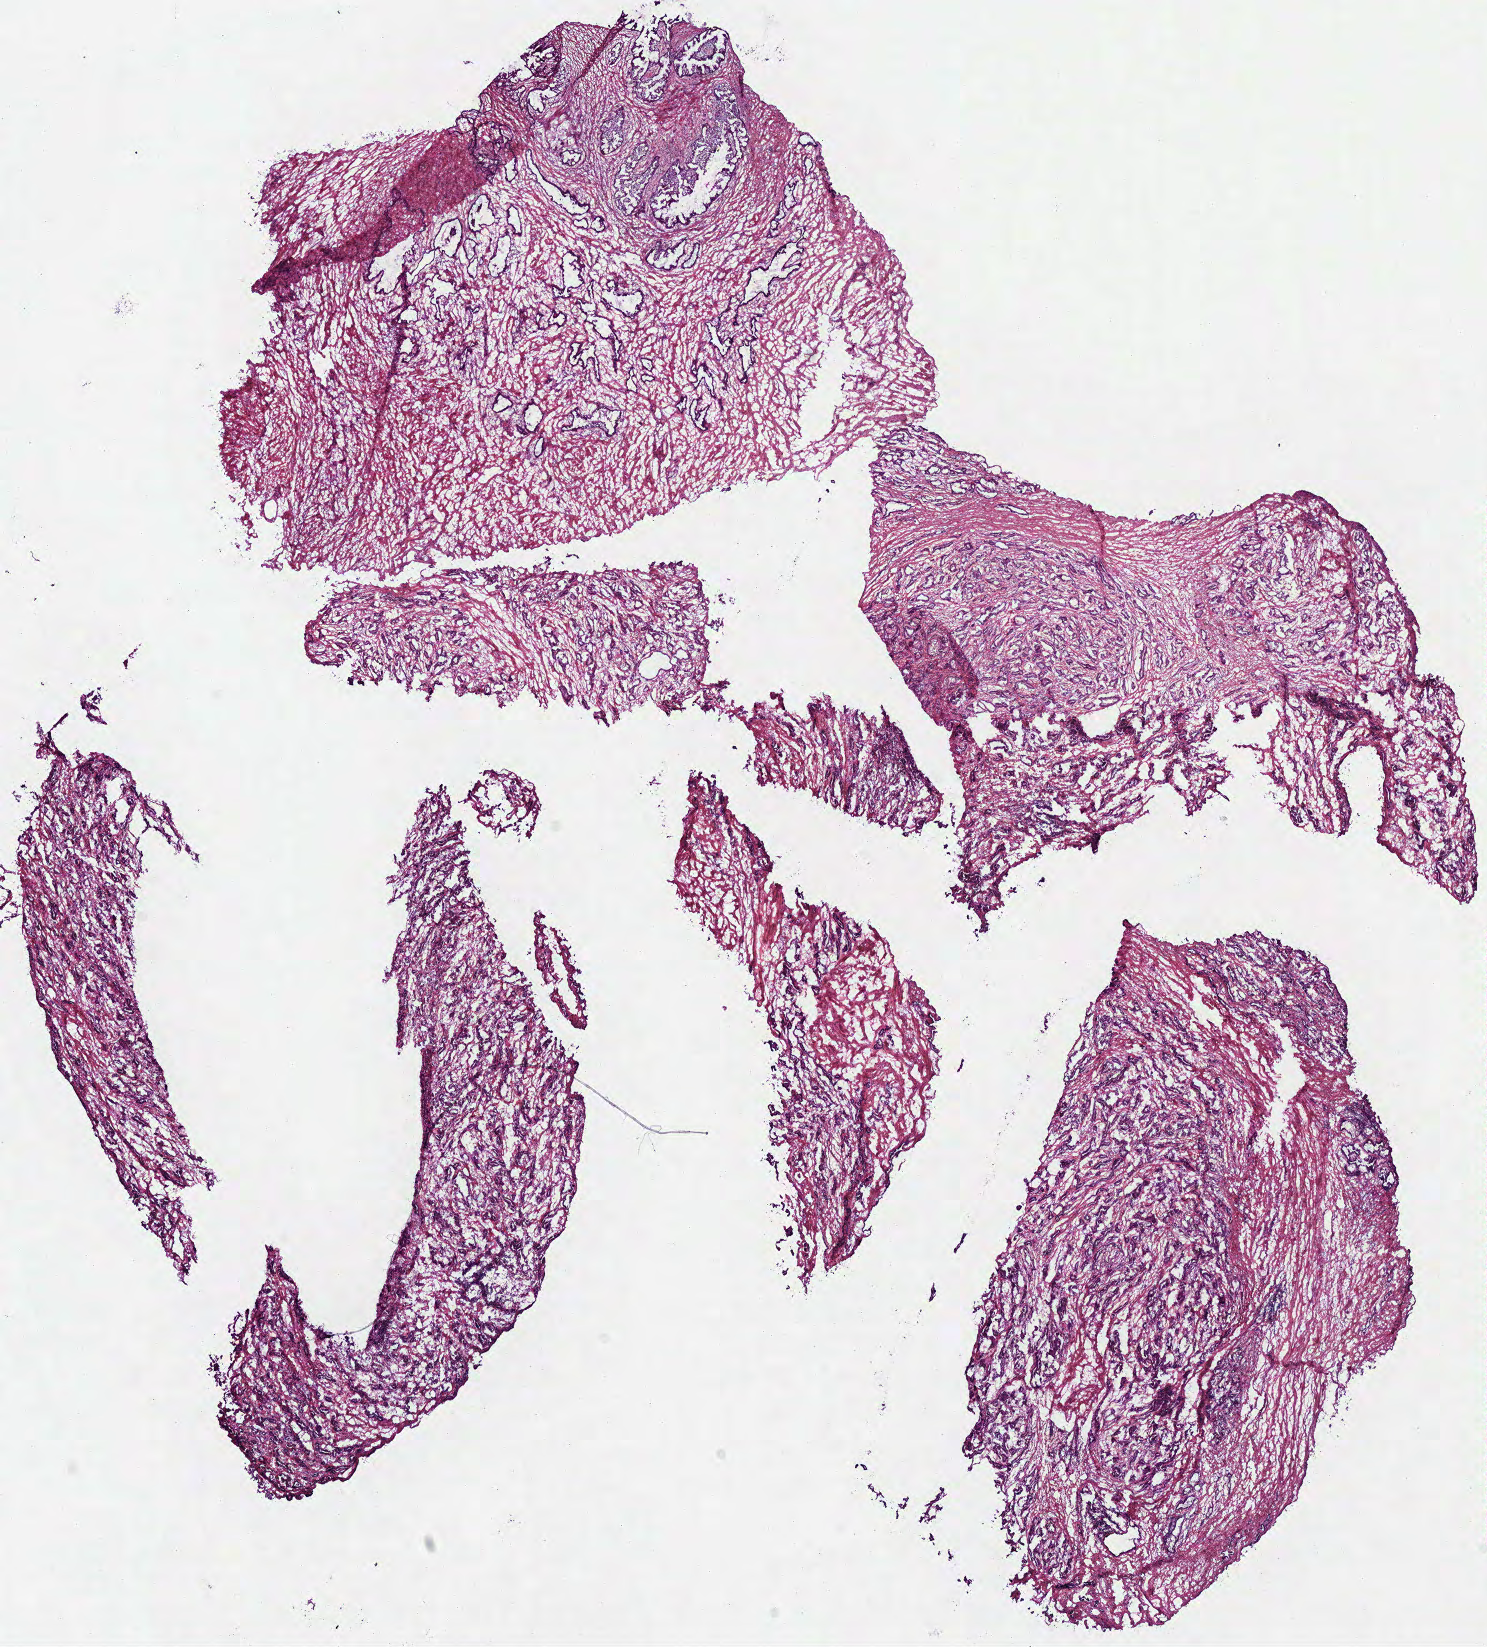
Digitized Hematoxylin and eosin (H&E) stained tissue section (whole slide) — a low-resolution overview of the entire scanned area, about 11.7 x 13.0 mm (from a 40x scan), frozen section from the bottom of the tissue portion, sample: primary tumour, prostate. Patient: male, age at initial diagnosis 58 years.
Diagnosis: Acinar cell carcinoma (prostate gland).